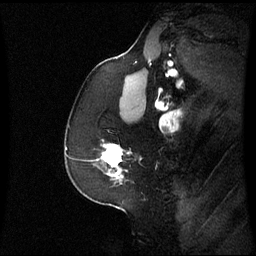
Breast MRI (dynamic contrast-enhanced), one sagittal slice. Position 43 of 60 along the scan axis. Dynamic contrast-enhanced series, image 2 of 3 at this slice position (ordered by acquisition). 1.5 T. TE 4.2 ms, TR 8.9 ms. 2.4 mm slice thickness. 256 × 256 image matrix, field of view 230 × 230 mm. Patient: female, 59 years. From the clinical record (not read from this slice): setting: breast cancer imaged before/during neoadjuvant chemotherapy; receptor status: triple-negative.
Structures marked on this image (semi-automatically segmented with operator editing):
- analysis volume of interest (the breast-tissue region the enhancement analysis was run in; not a lesion): bounding box (x1, y1, x2, y2) in pixels: (97, 140, 124, 182)
- tumour enhancement mask (voxels above the 70 % enhancement threshold inside the analysis volume of interest): (102, 144, 123, 177)